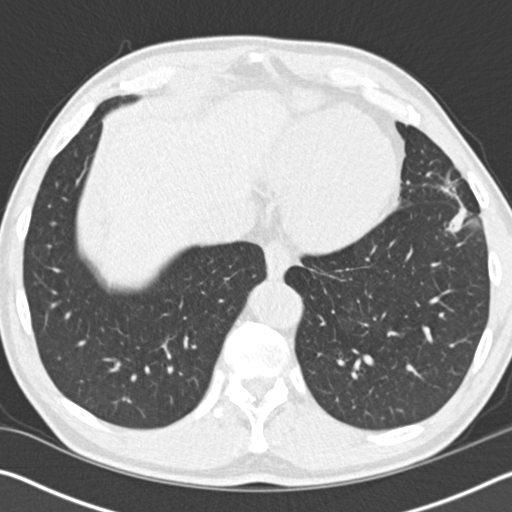
Low-dose screening chest CT, one axial slice; slice 38 of 162 in the series (ordered by position); 120 kVp; lung window (W 1500 / L -600 HU); 2 mm slice thickness; 512 × 512 image matrix, field of view 340 × 340 mm.
Annotated regions visible in this slice (manually delineated by an expert):
- lesion 1 (tumor, upper lobe of left lung): bounding box <441,185,467,233> (left, top, right, bottom; pixels)